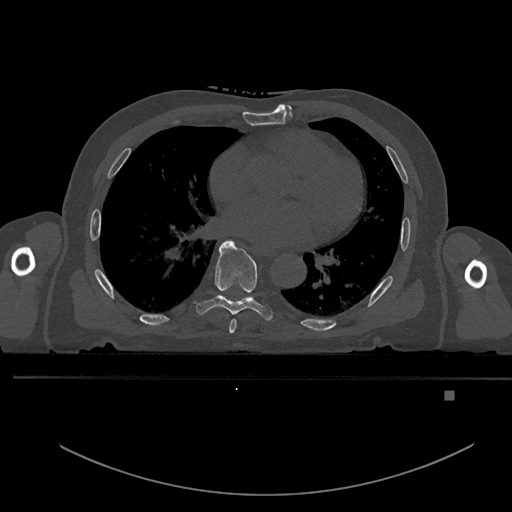
CT including the spine, one axial slice. Slice 255 of 969 in the series (ordered by position). Bone window (W 1800 / L 400 HU). 512 × 512 image matrix, field of view 456 × 456 mm. Male patient, age 82 years. From the clinical record (not read from this slice): primary cancer: prostate; vertebrae with lytic lesions (as recorded): T11, T9, T8, T2.
Outlined on this slice (semi-automatic segmentation, software-assisted and operator-edited):
- T6 vertebra: bounding box [x1, y1, x2, y2] px = [229, 319, 237, 334]
- T7 vertebra: [195, 240, 273, 321]
- T8 vertebra: [225, 295, 255, 301]